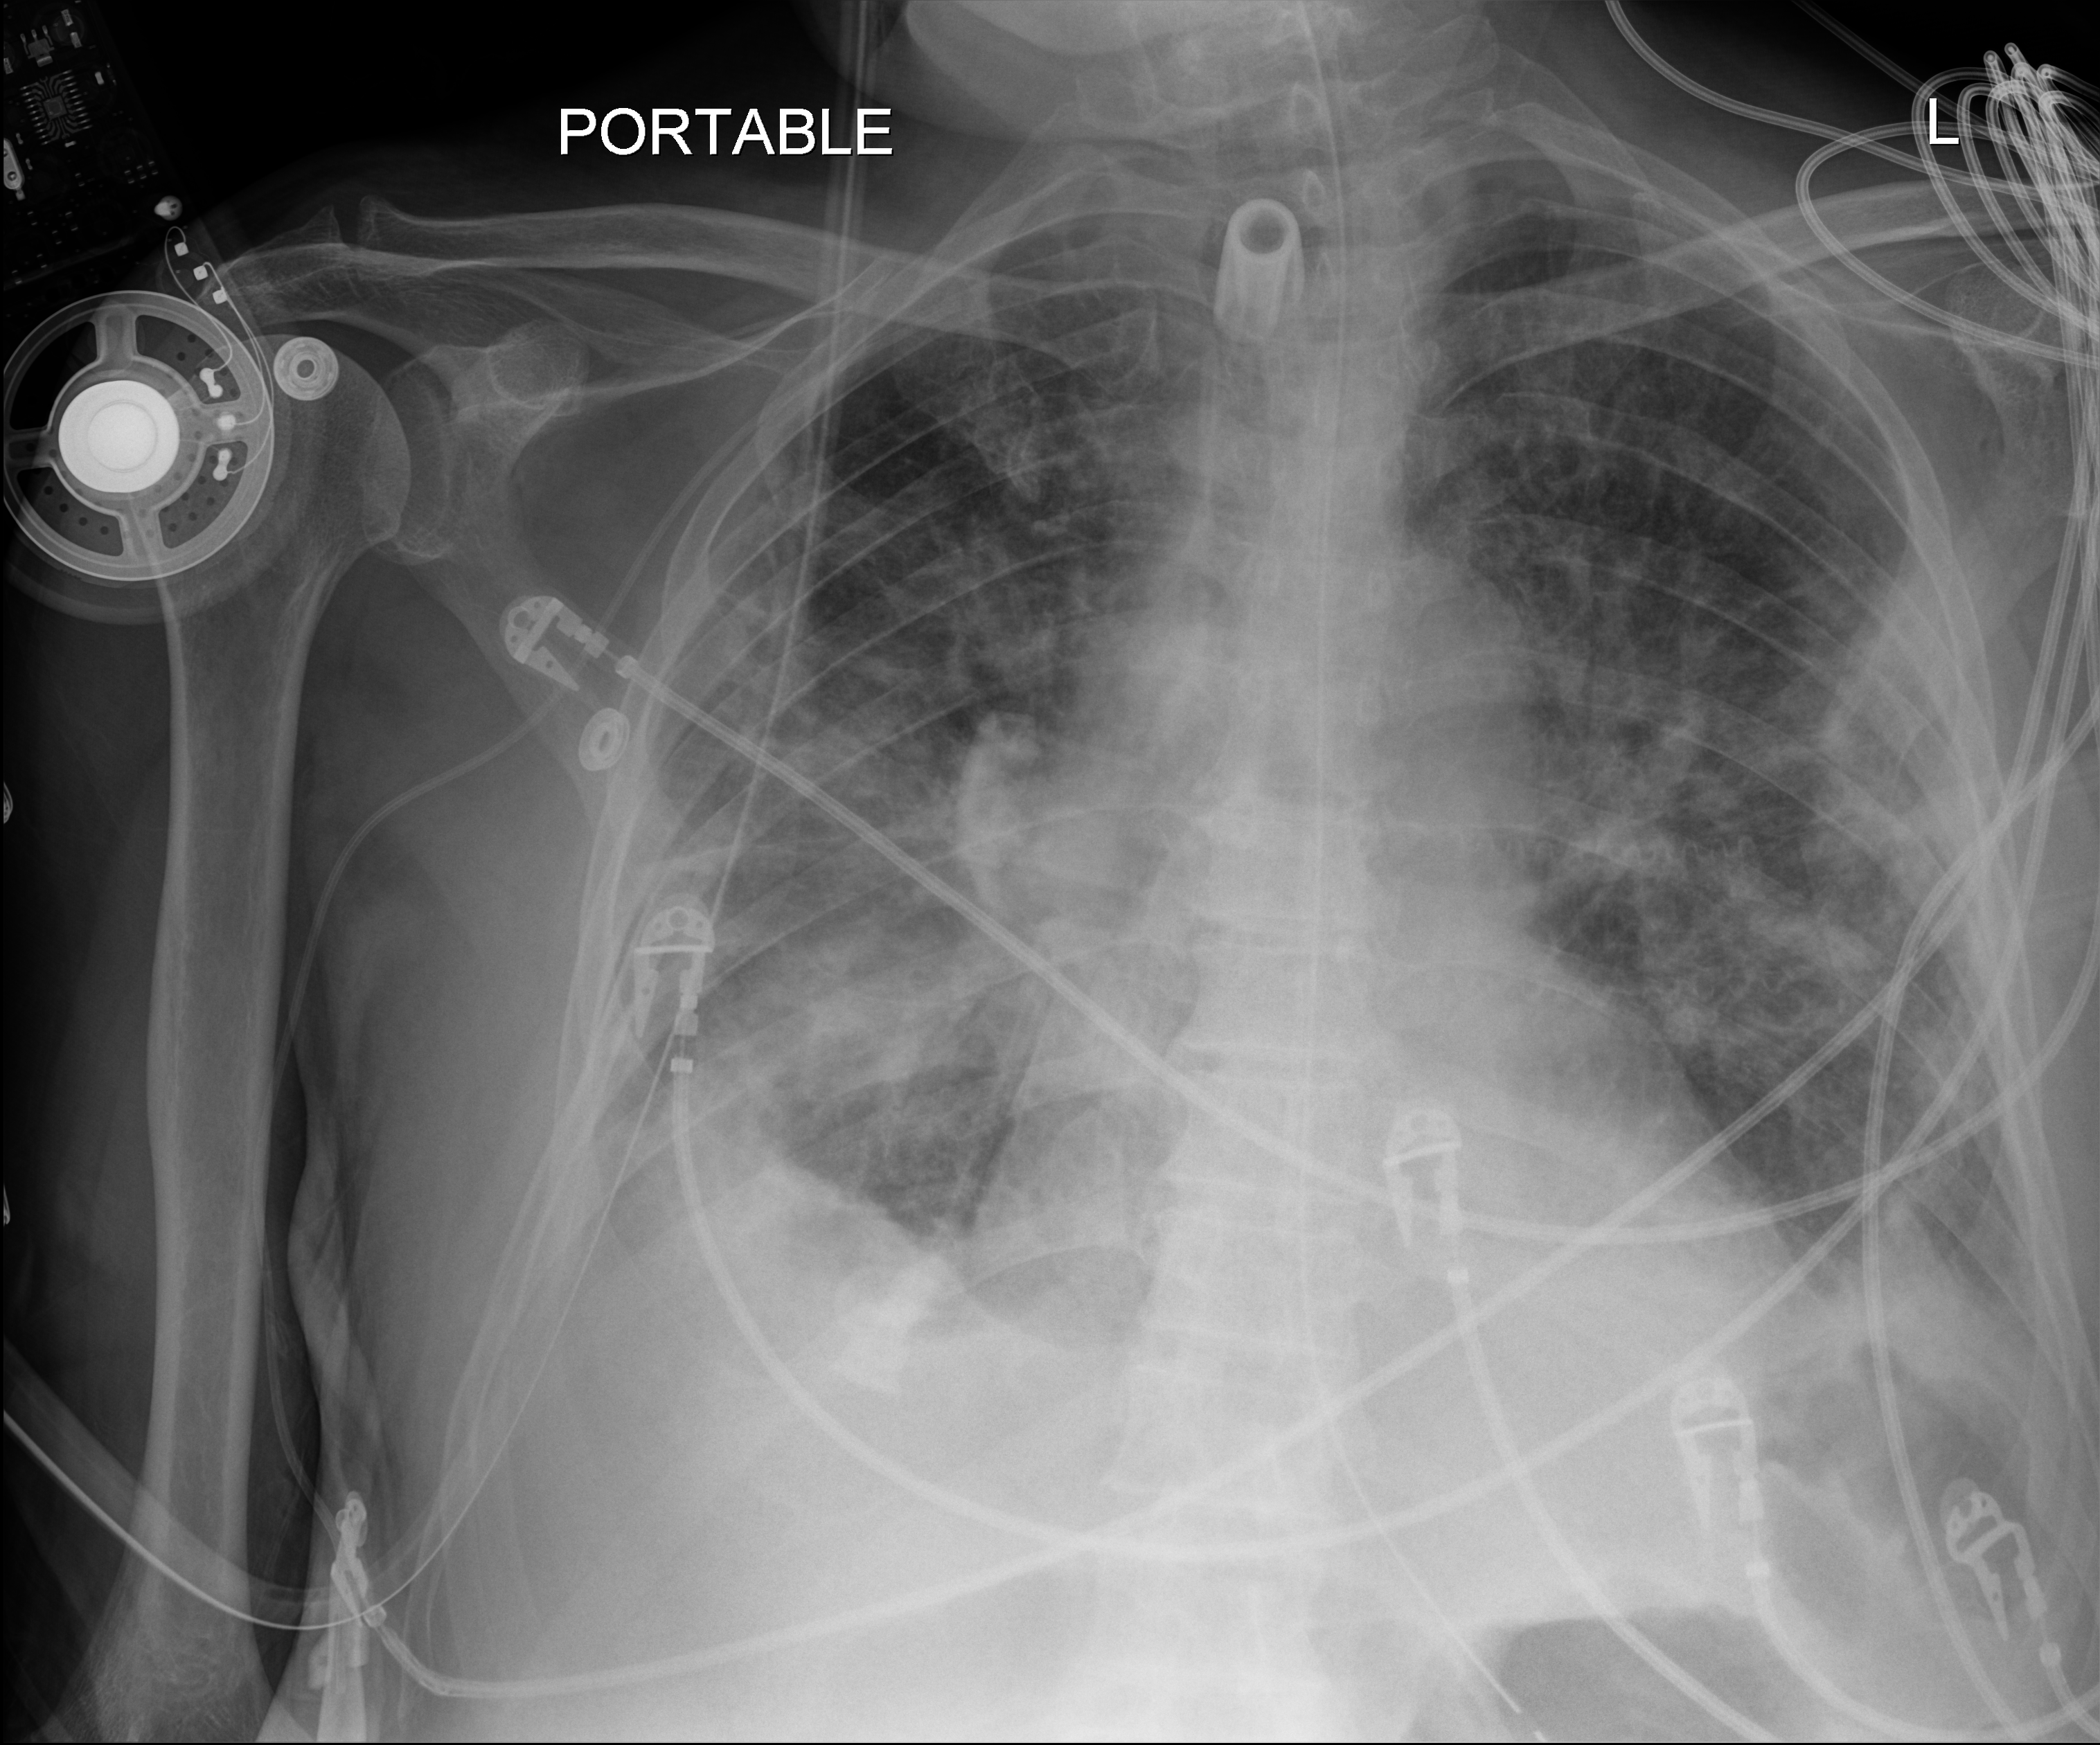
Bedside chest radiograph (digital radiography), anteroposterior (AP) projection. Male patient hospitalised with COVID-19, age 75–90 years.
Hospital-stay facts (about this admission, not read from this image; timing relative to this image not recorded): mechanically ventilated during this hospital stay: yes; length of hospital stay: 70 days.